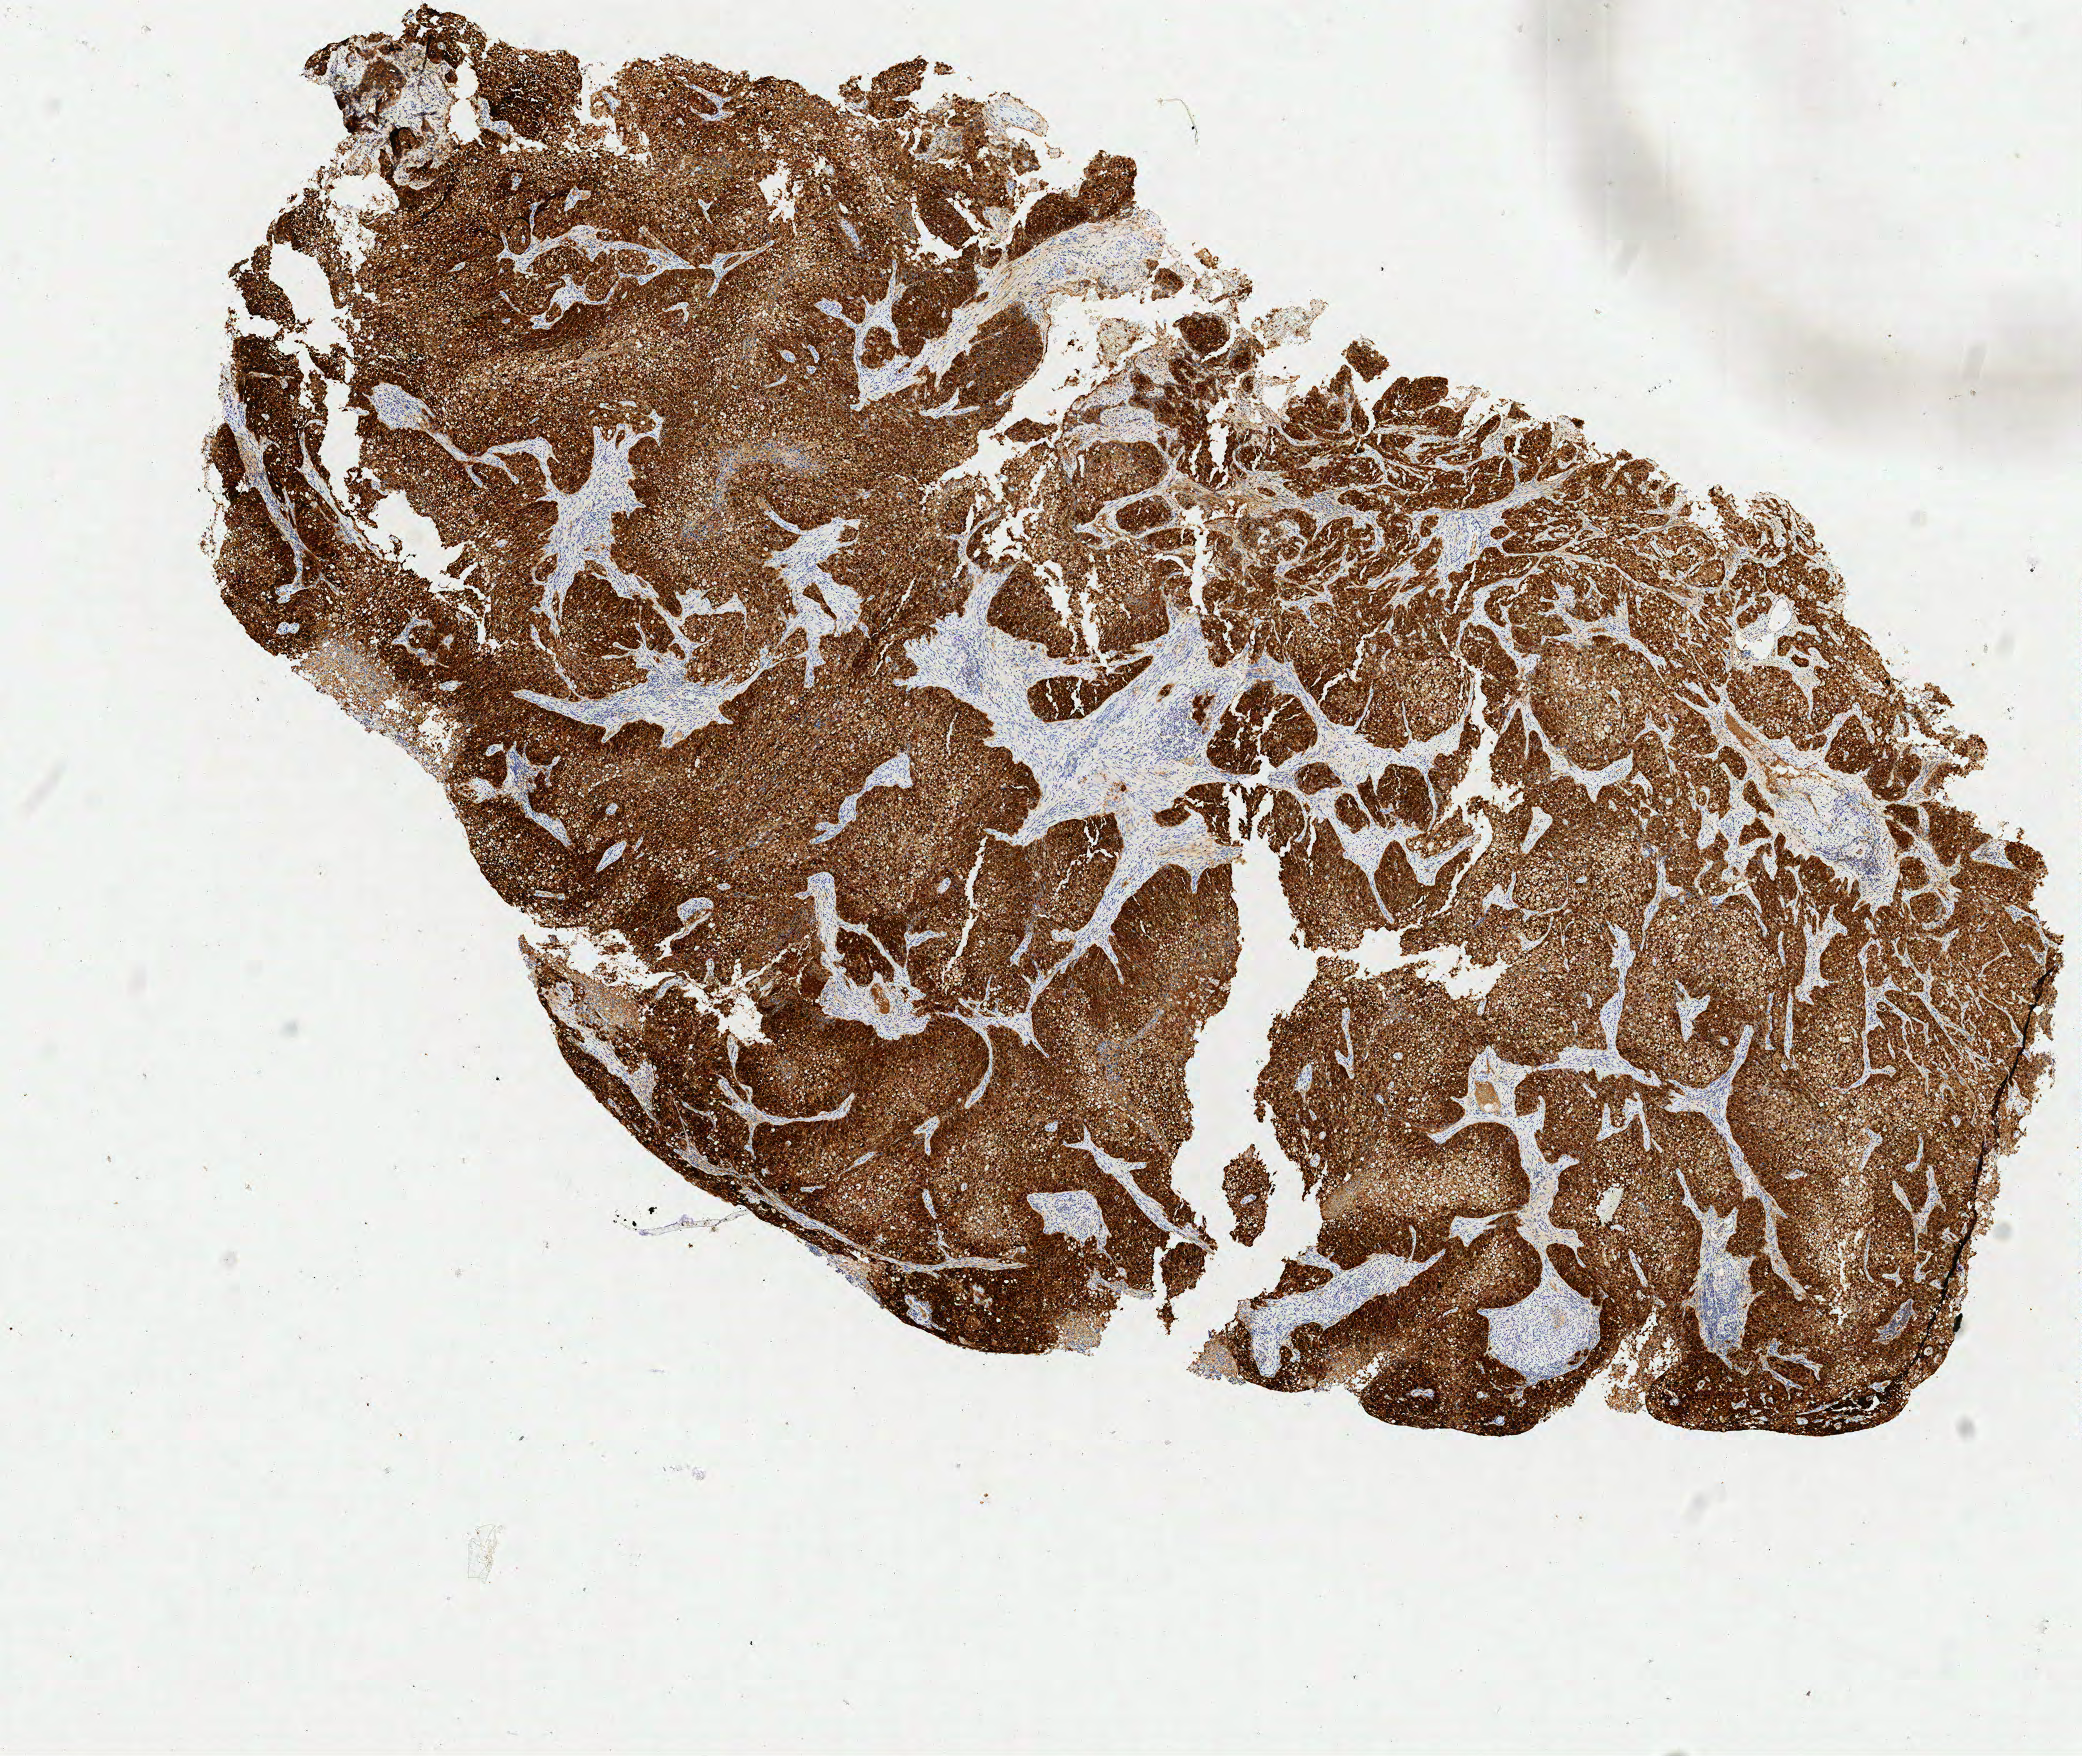
Immunohistochemistry (IHC) whole-slide image stained for p16 (p16INK4a) — low-resolution overview of the scanned area, about 8.3 x 7.0 mm. Specimen: tumor tissue. Anatomic site: cervix. Female patient, age 39 years.
* histologic diagnosis: Squamous cell carcinoma, large cell, nonkeratinizing, NOS